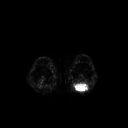
FDG PET of an extremity soft-tissue mass (from a PET/CT study), one axial slice. 128 × 128 image matrix, field of view 500 × 500 mm. Male patient, age 54 years. Case-level facts recorded for this patient, not image findings: histological type: synovial sarcoma; site of the primary tumour: left poplietal fossa.
Outlined on this slice (expert contour drawn on MRI and transferred to this co-registered scan by the dataset authors):
- gross tumour volume (mass): bounding box <74,82,89,92> (left, top, right, bottom; pixels)